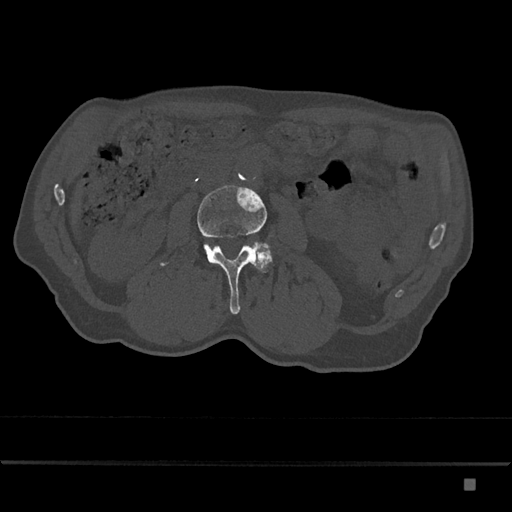
CT including the spine, one axial slice. Slice 400 of 797 in the series (ordered by position). Reconstruction kernel Br40s/3. 120 kVp. Bone window (W 1800 / L 400 HU). 512 × 512 image matrix, field of view 390 × 390 mm. Patient: male, 72 years. From the clinical record (not read from this slice): primary cancer: prostate.
Annotated regions visible in this slice (semi-automatic segmentation, software-assisted and operator-edited):
- L3 vertebra: bounding box [x1, y1, x2, y2] px = [160, 185, 270, 314]
- L4 vertebra: [256, 247, 272, 272]